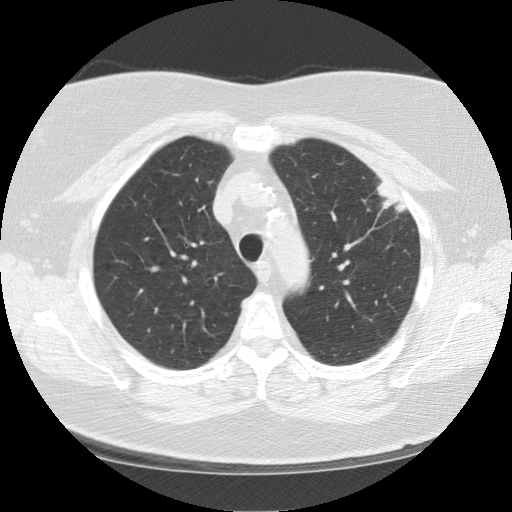
Low-dose screening chest CT, axial slice. First (baseline) screen. Lung window (W 1500 / L -600 HU). 2.5 mm slice thickness. Standard (soft-tissue) reconstruction kernel (STANDARD). 120 kVp. Female, age 67 years at enrolment. Former smoker at enrolment.
- Lesion marked by an expert reader, bounding box (x1, y1, x2, y2) in pixels: (351, 165, 420, 227).
- Reader record for this screening exam (exam-level; its link to the box is not recorded): non-calcified nodule or mass ≥4 mm, left upper lobe, 28 × 19 mm, soft tissue attenuation.
- Official screen result: positive, change unspecified: nodule(s) >= 4 mm or enlarging nodule(s), mass(es), or other non-specific abnormalities suspicious for lung cancer.